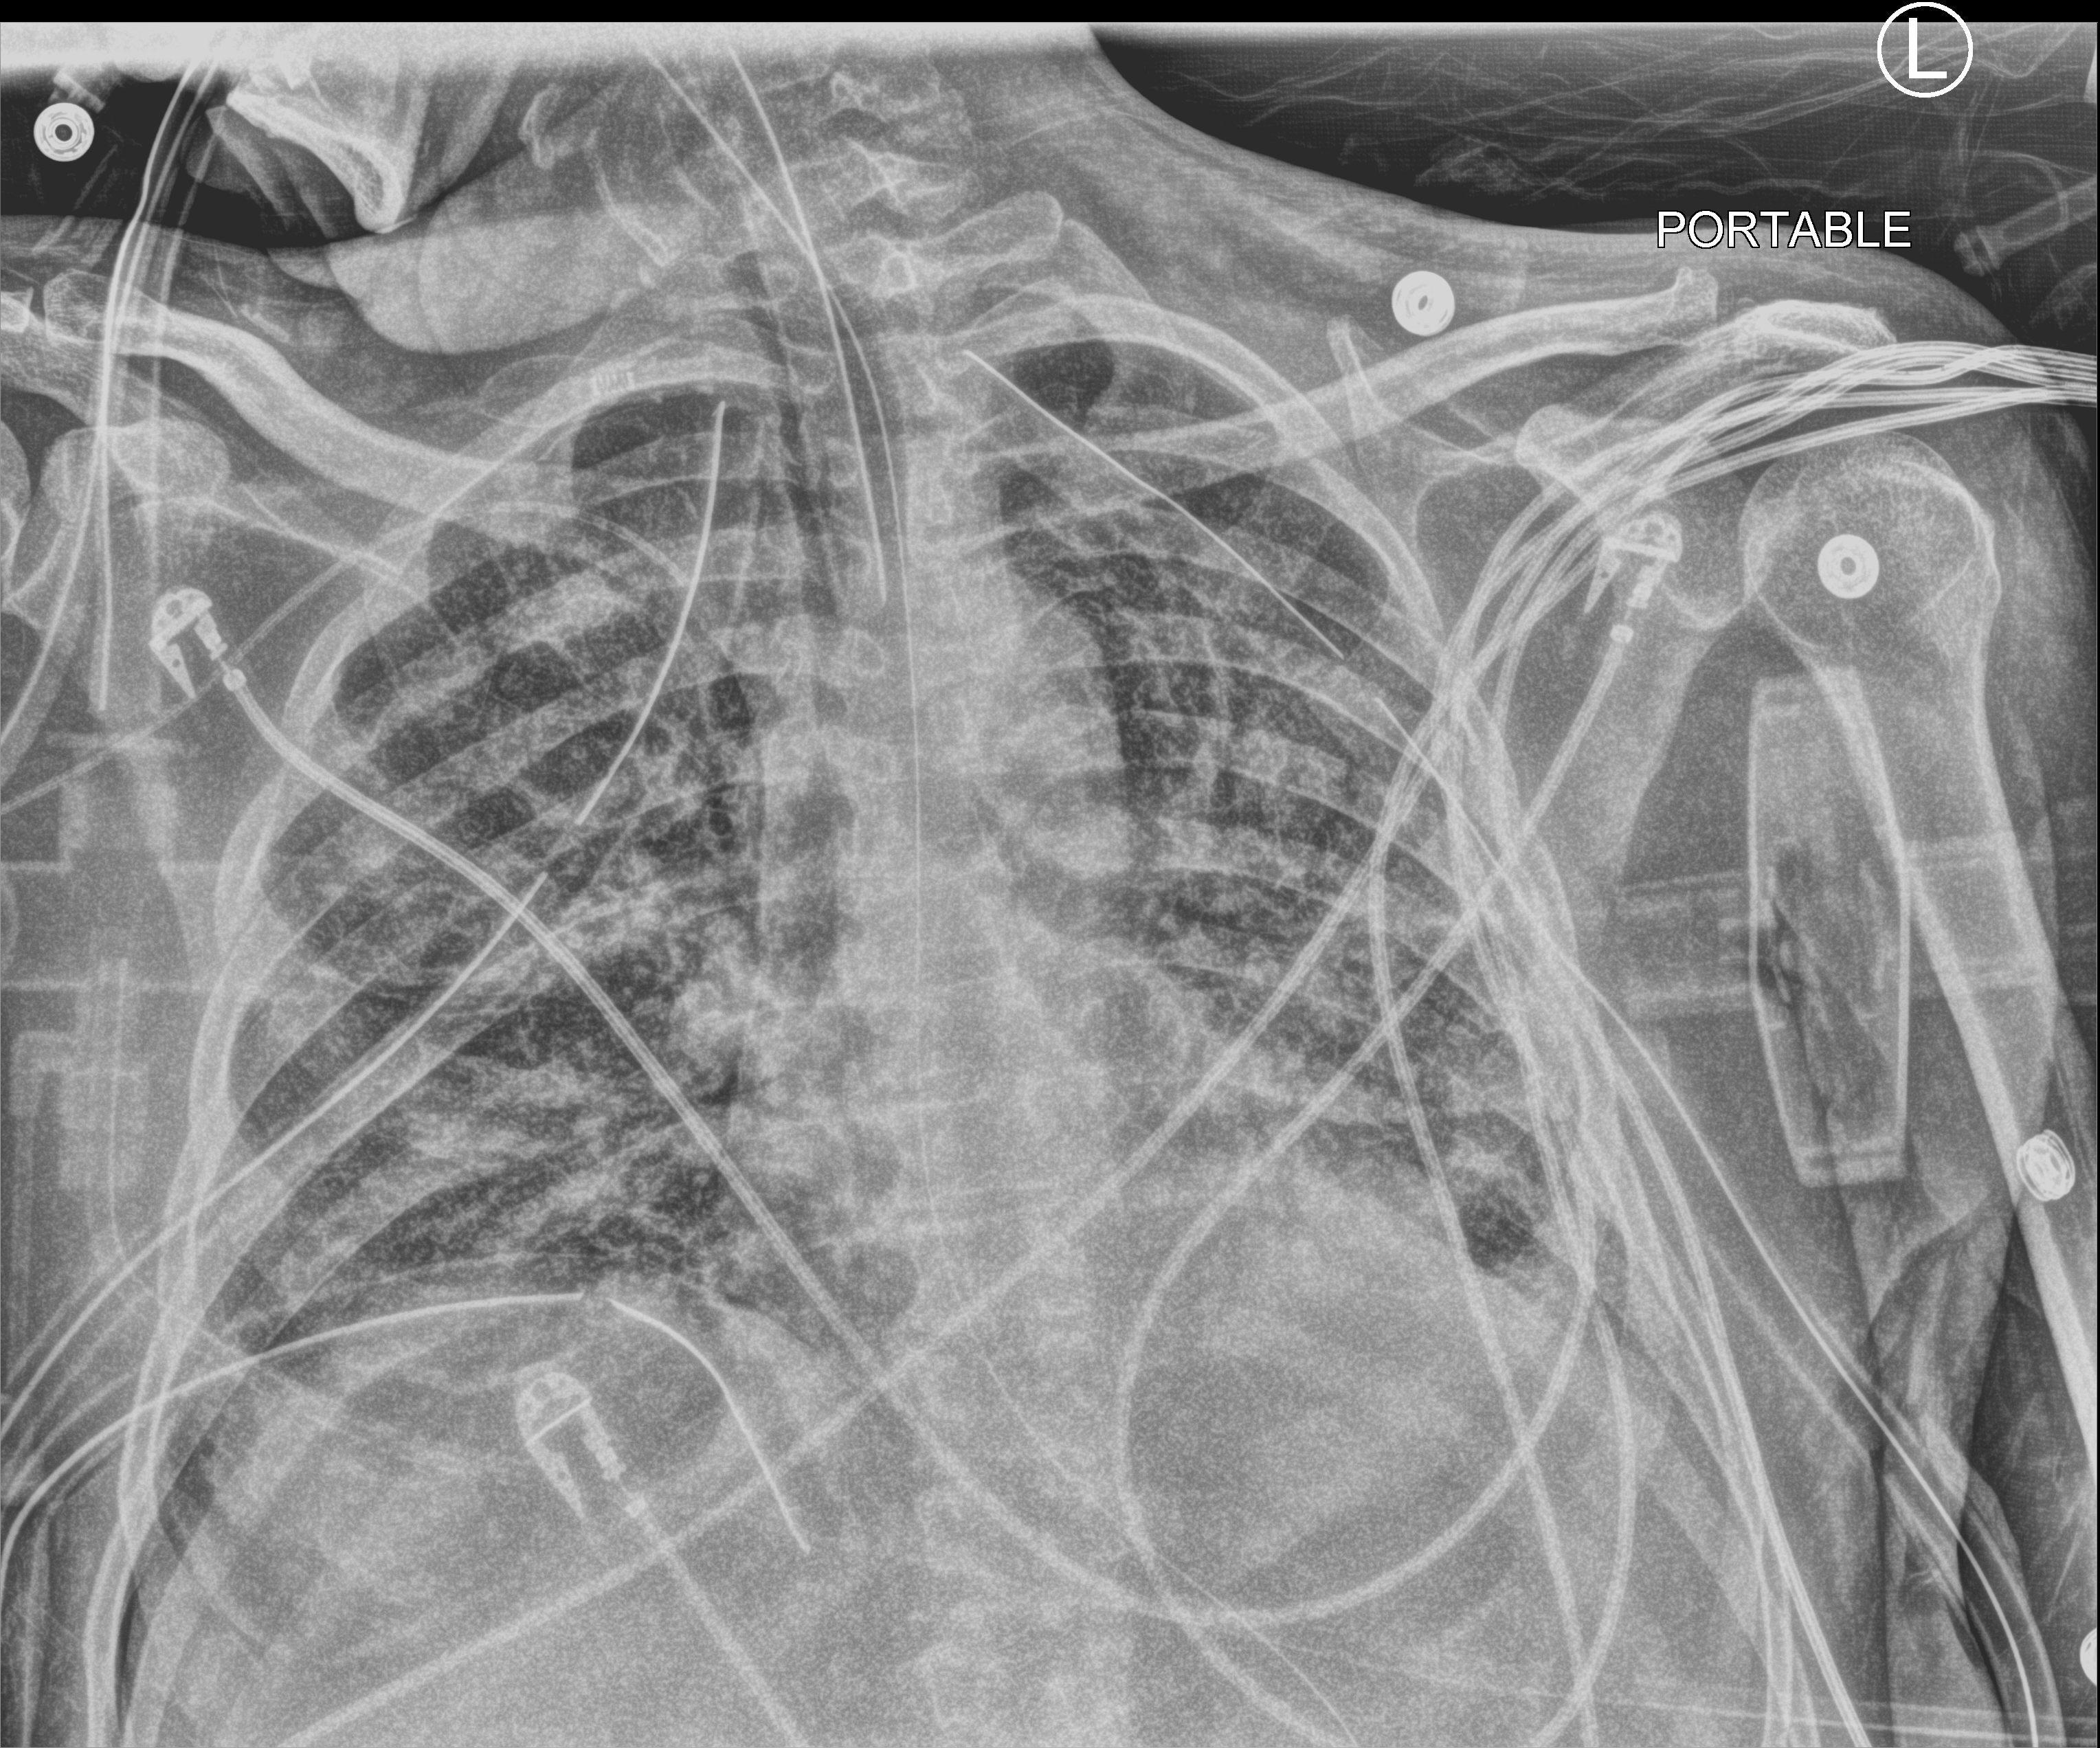
Portable chest radiograph. Patient hospitalised with COVID-19; male, aged 18–59 years.
Hospital-stay facts (about this admission, not read from this image; timing relative to this image not recorded): mechanically ventilated during this hospital stay: yes; admitted to intensive care during this hospital stay: yes; hypertension (admission record): yes.